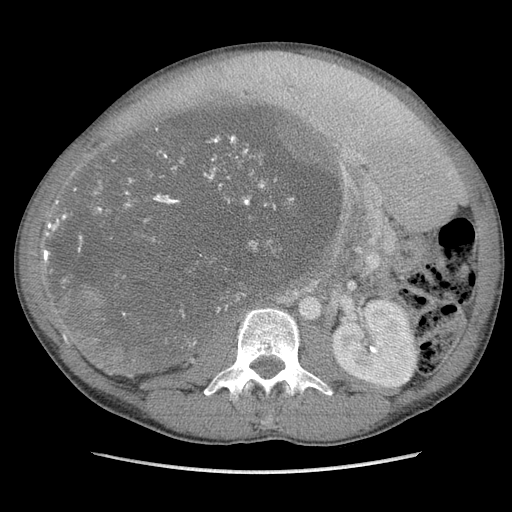
Contrast-enhanced abdominal CT, one axial slice; slice 57 of 115 in the series (ordered by position); soft-tissue window (W 400 / L 40 HU); 512 × 512 image matrix, field of view 360 × 360 mm. Male patient. Case-level facts recorded for this patient, not image findings: diagnosis: adrenocortical carcinoma; tumour side: right adrenal; Ki-67 index: 13 %; stage (as recorded): 3.
Structures marked on this image (semi-automatic segmentation, software-assisted and operator-edited):
- mass: box from (x=54, y=102) to (x=341, y=374) px